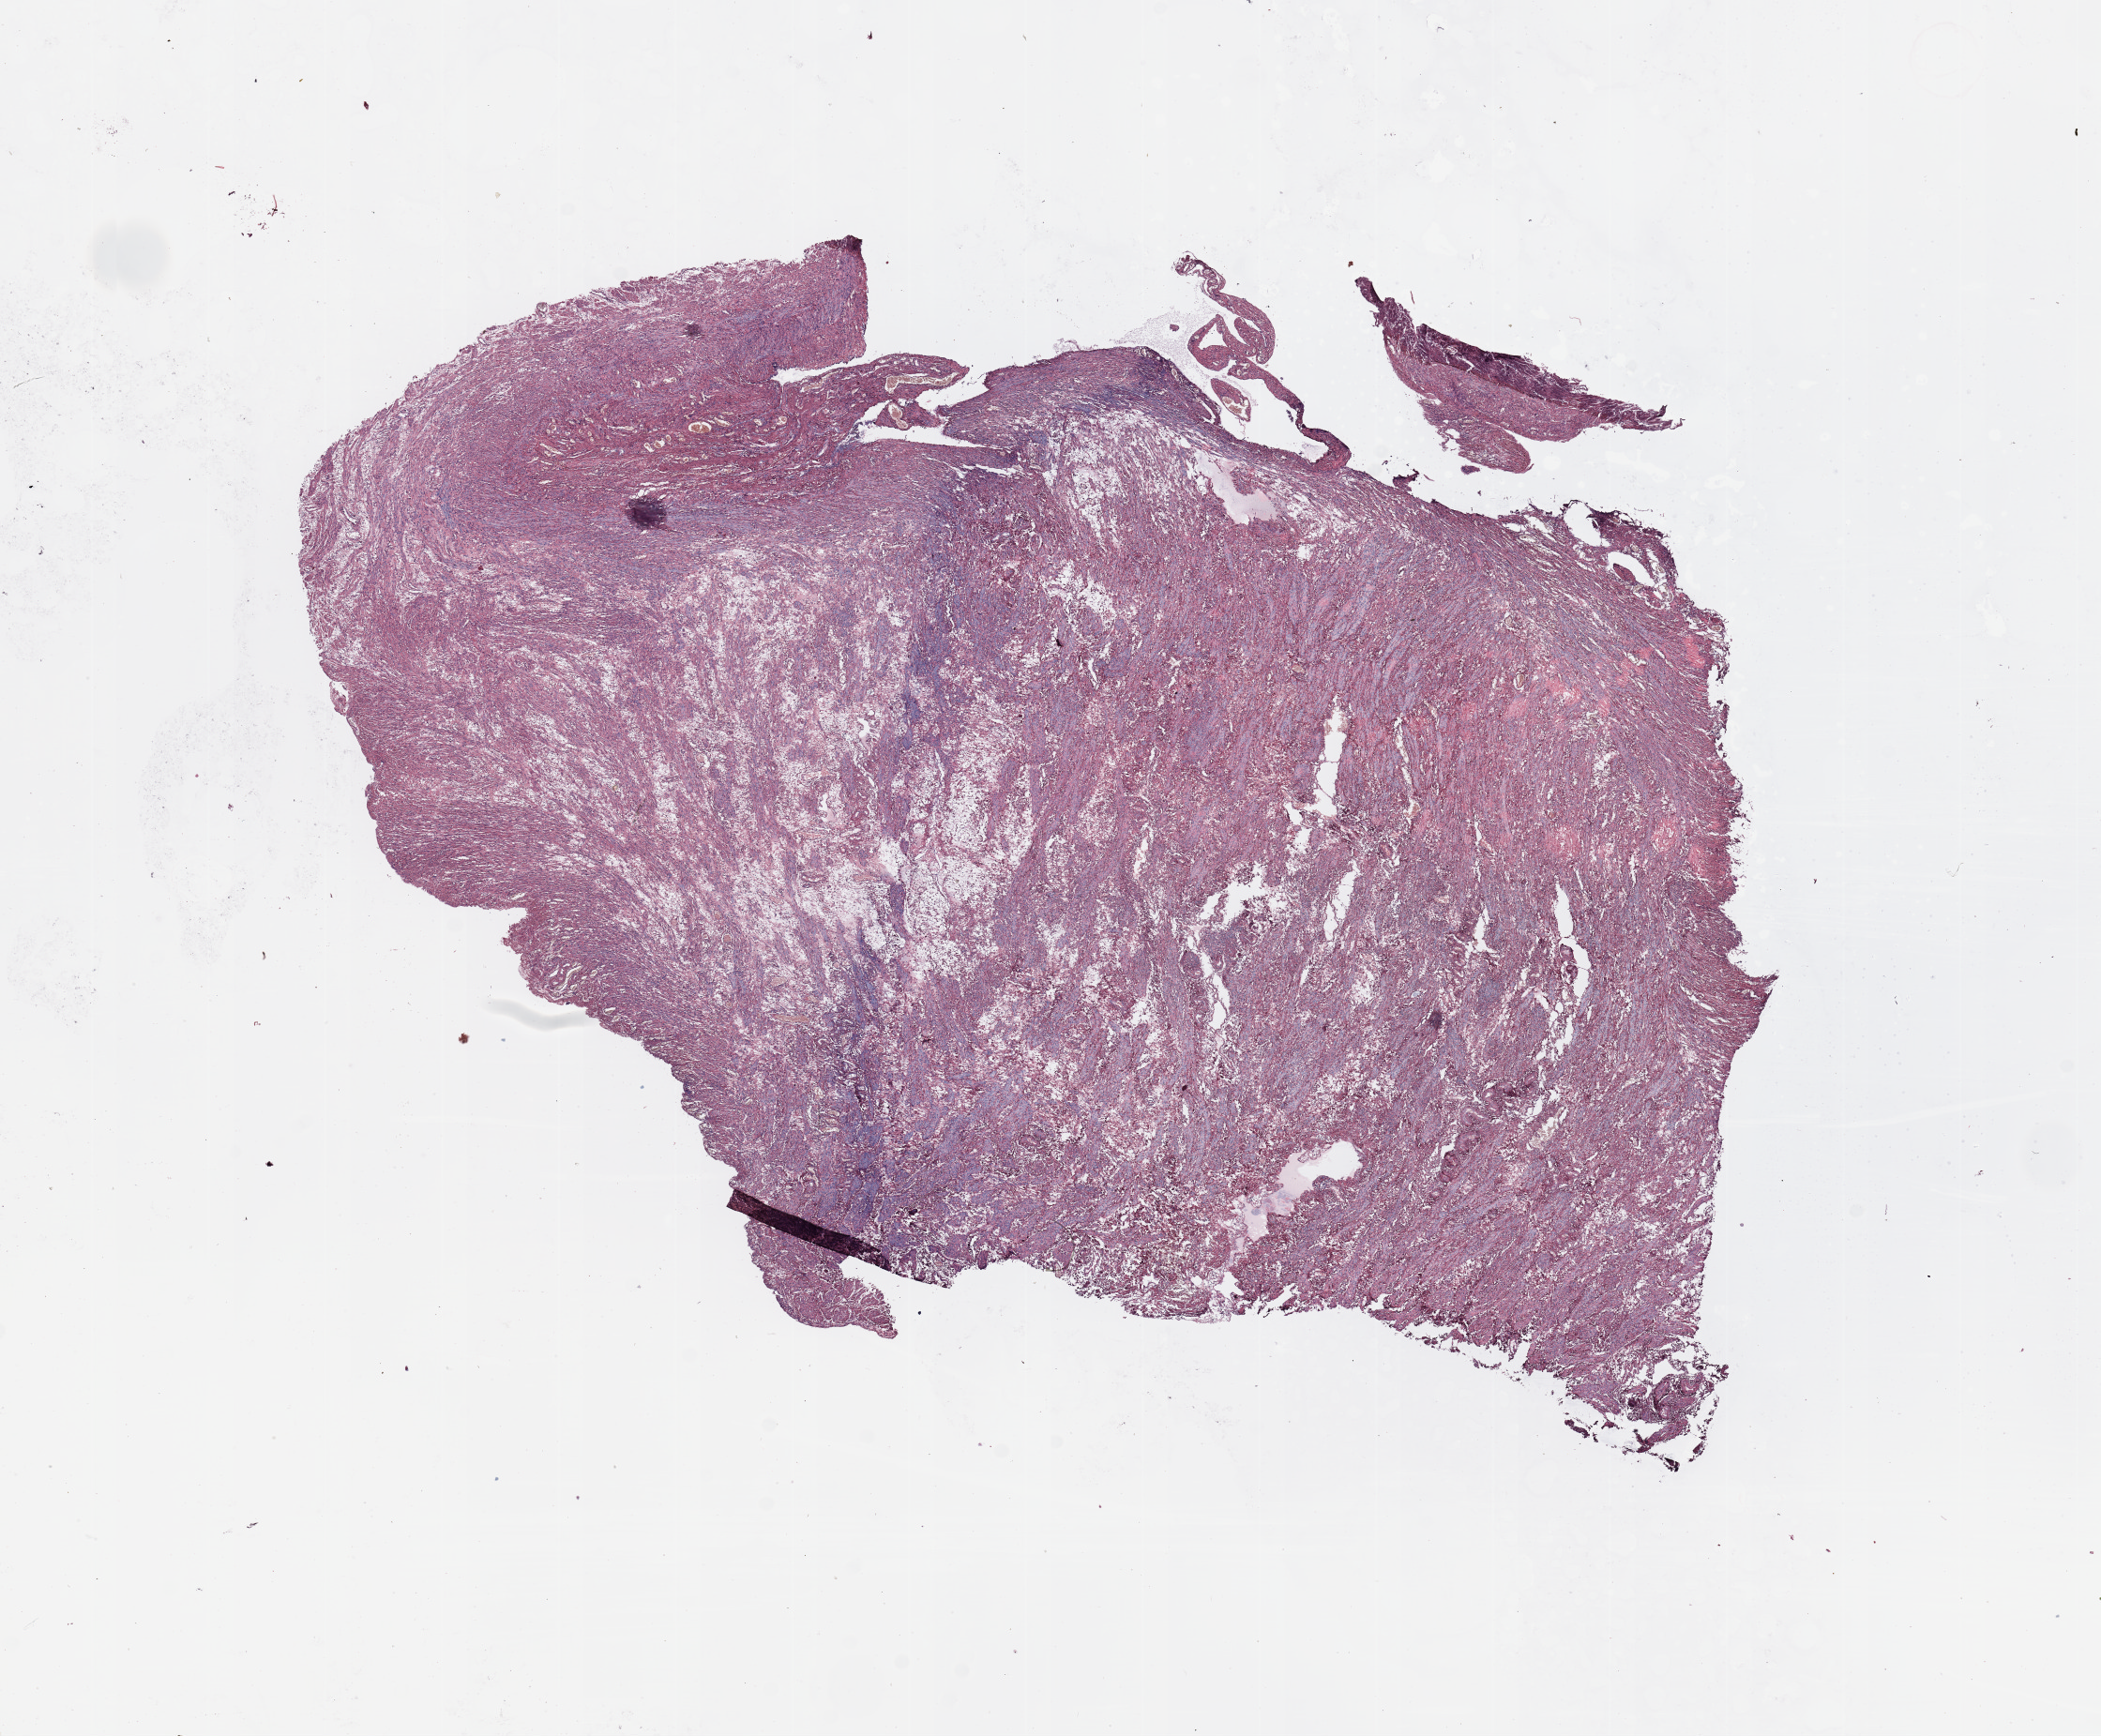
Whole-slide histology image, Hematoxylin and eosin (H&E) stained — a low-resolution overview of the entire scanned area, about 17.7 x 14.6 mm (slide scanned at 20x). Uterus, normal (non-tumour) tissue. Female, 59 y/o.
* this section: normal (non-tumour) tissue from the same patient
* patient diagnosis: Endometrioid adenocarcinoma, NOS